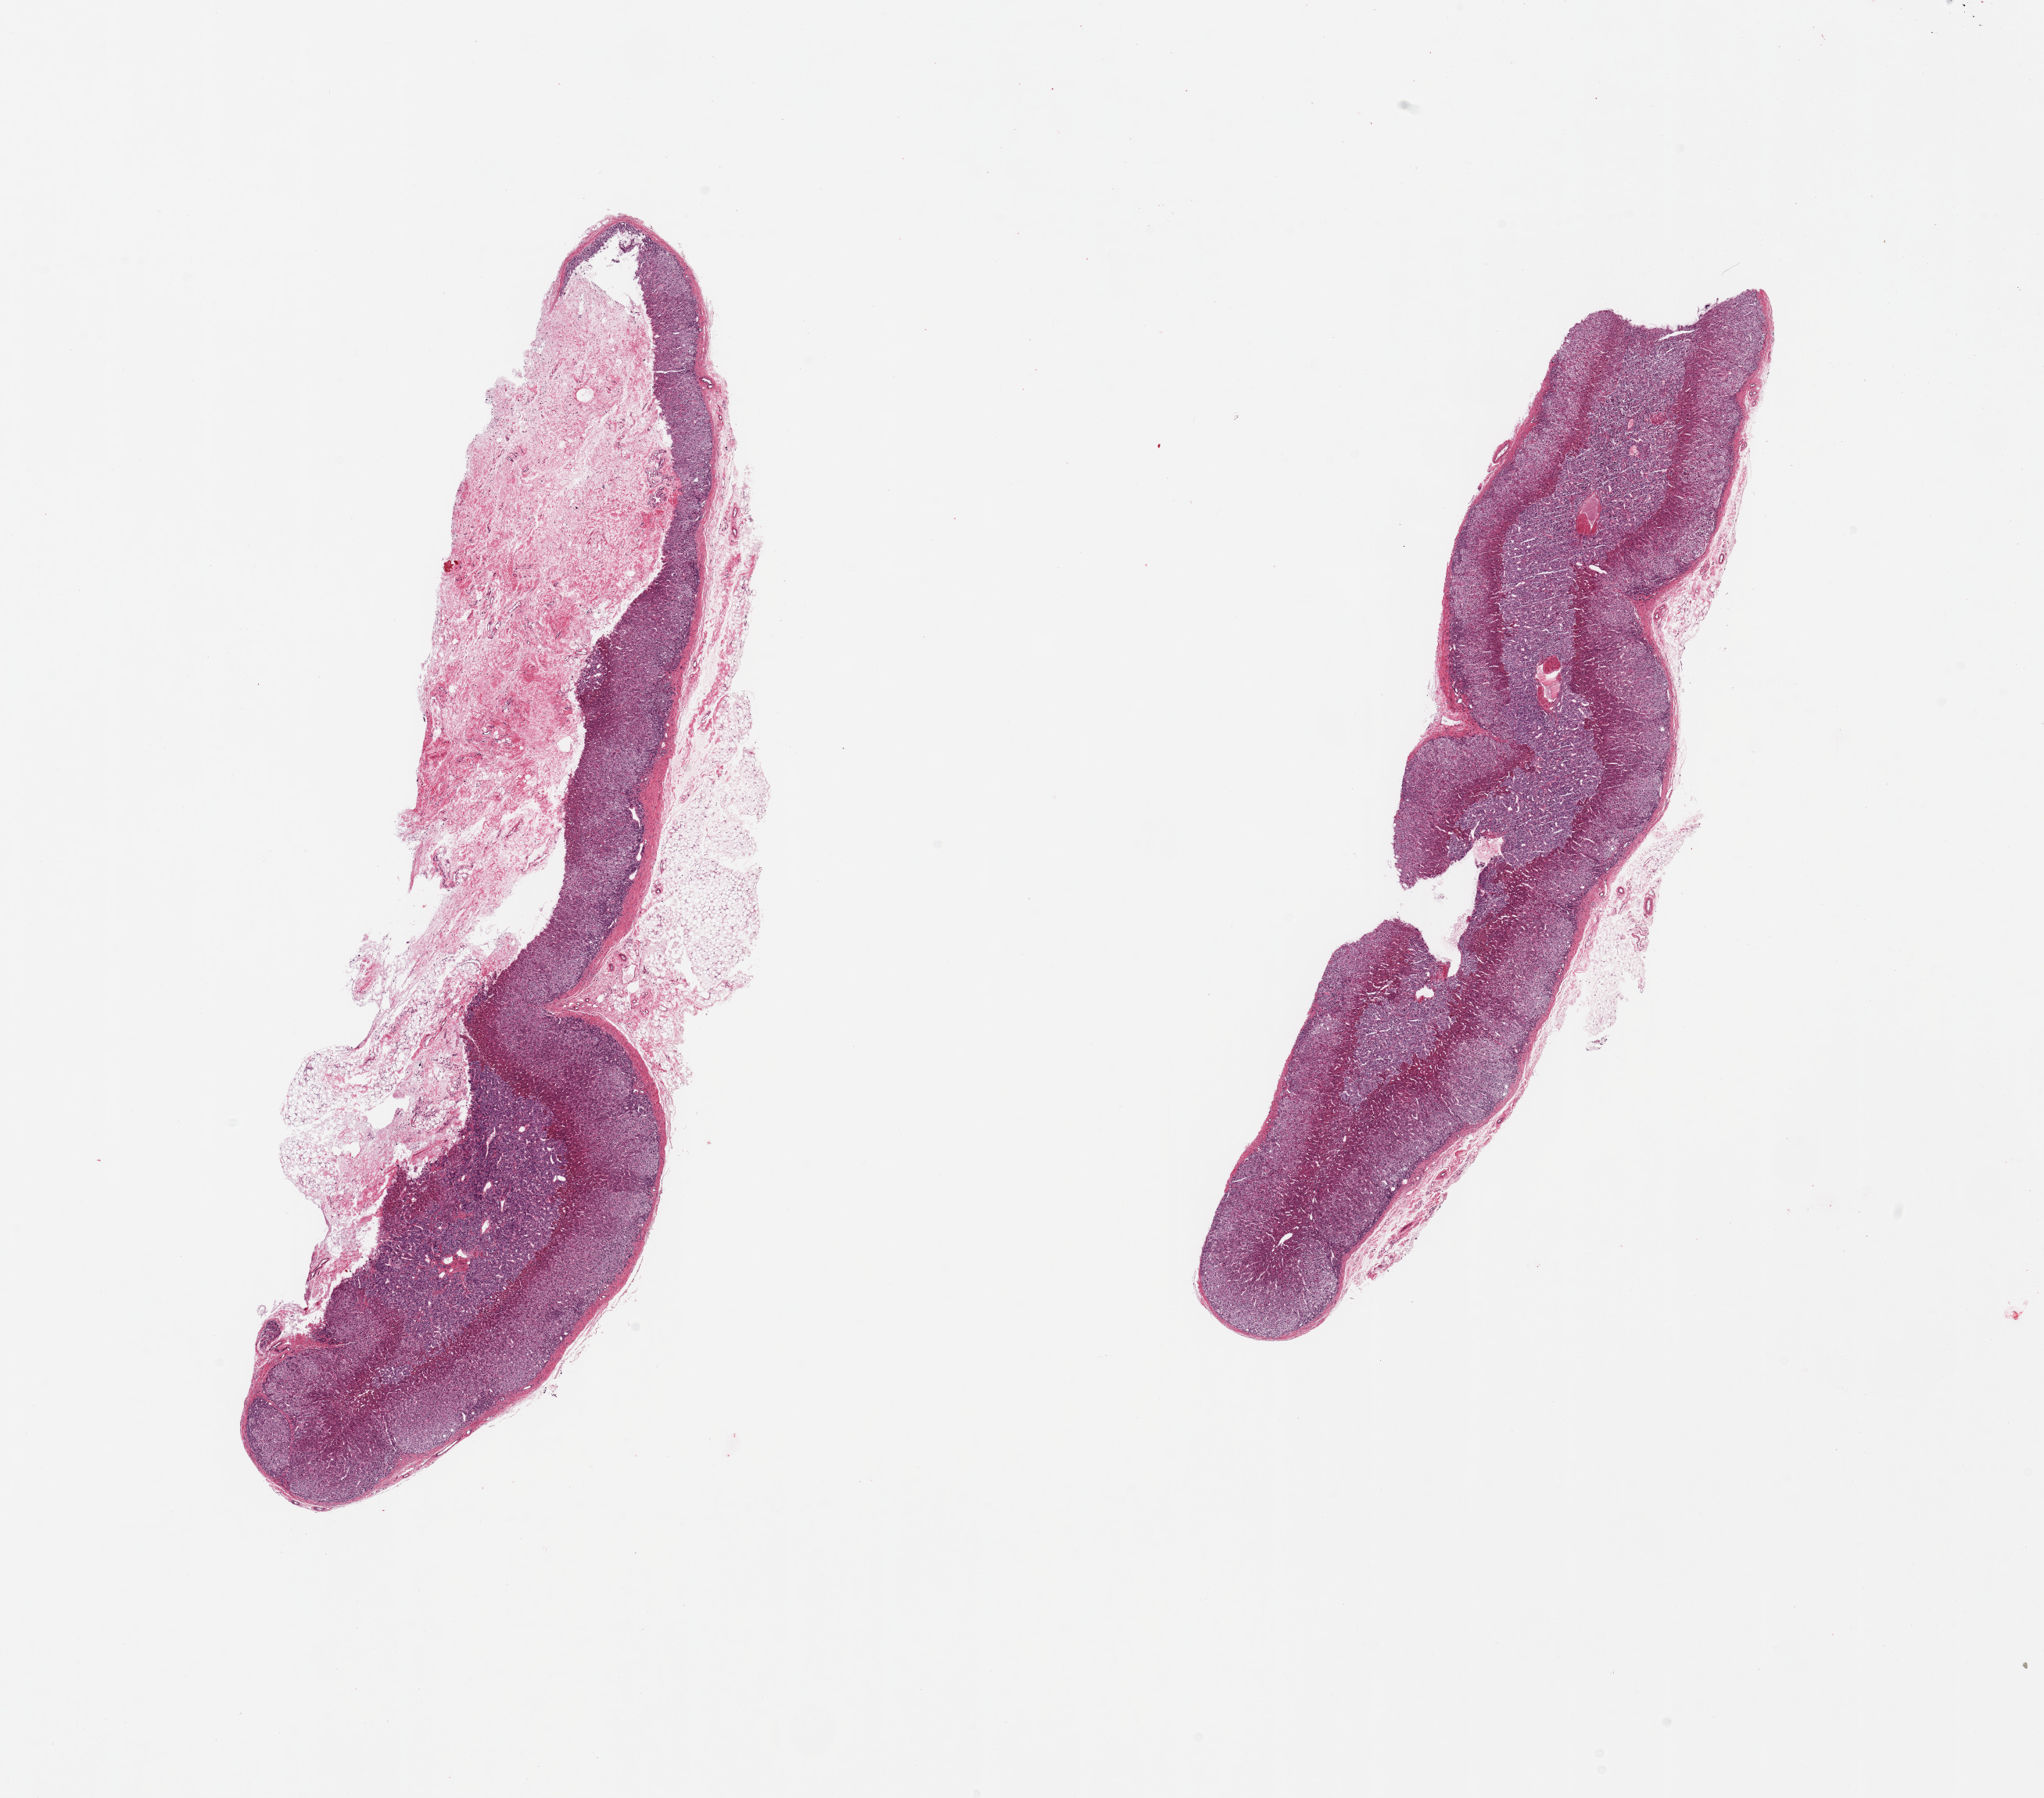
Whole-slide image, haematoxylin and eosin stain, whole scanned area (about 20.7 x 18.2 mm) shown as a low-resolution overview, PAXgene-fixed paraffin-embedded (PFPE) section, sampled site (target tissue): adrenal gland, tissue donor sample. Female donor.
- review note (as recorded): 2 pieces; possible medullary hyperplasia, residual attached fat